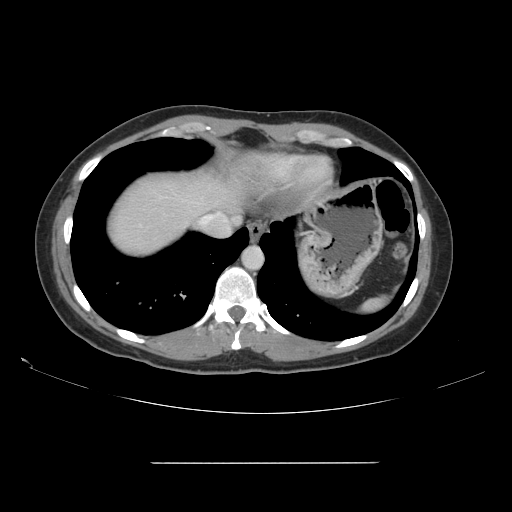
Contrast-enhanced abdominal CT, one axial slice; slice 137 of 151 in the series (ordered by position); 120 kVp; intravenous contrast given; soft-tissue window (W 400 / L 40 HU); 512 × 512 image matrix, field of view 421 × 421 mm. Female patient, age 46 years. From the clinical record (not read from this slice): diagnosis: colorectal cancer liver metastases, imaged before liver resection; multiple liver metastases: yes; largest metastasis: 3 cm.
Structures marked on this image (outlined manually by an expert reader):
- hepatic veins: bounding box (x1, y1, x2, y2) in pixels: (200, 213, 220, 225)
- liver: (106, 172, 240, 256)
- planned liver remnant (the part of the liver to remain after resection): (121, 173, 240, 230)